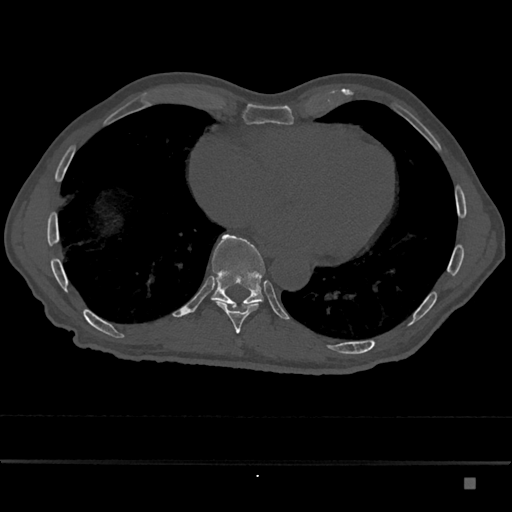
CT including the spine, one axial slice. Position 777 of 797 along the scan axis. Reconstruction kernel Br40s/3. Bone window (W 1800 / L 400 HU). 0.5 mm slice thickness. 512 × 512 image matrix. Male patient, age 72 years. Case-level facts recorded for this patient, not image findings: primary cancer: prostate.
Structures marked on this image (semi-automatically segmented with operator editing):
- T10 vertebra: box from (x=211, y=234) to (x=265, y=309) px
- T9 vertebra: (x=217, y=303)–(x=258, y=334)